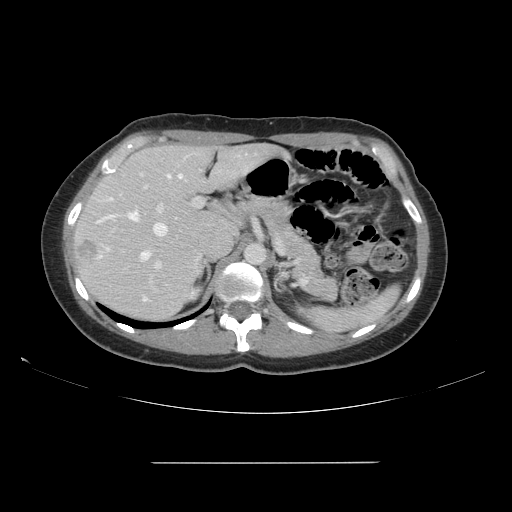
Contrast-enhanced abdominal CT, one axial slice. Position 102 of 151 along the scan axis. 120 kVp. Intravenous contrast given. Soft-tissue window (W 400 / L 40 HU). 512 × 512 image matrix, field of view 421 × 421 mm. Female patient, age 46 years. Case-level facts recorded for this patient, not image findings: diagnosis: colorectal cancer liver metastases, imaged before liver resection; multiple liver metastases: yes; largest metastasis: 3 cm.
Annotated regions visible in this slice (outlined manually by an expert reader):
- hepatic veins: bounding box <96,174,183,261> (left, top, right, bottom; pixels)
- liver: <73,144,277,321>
- planned liver remnant (the part of the liver to remain after resection): <89,146,279,255>
- portal vein (with intrahepatic branches): <140,173,203,301>
- liver metastasis: <77,241,98,260>